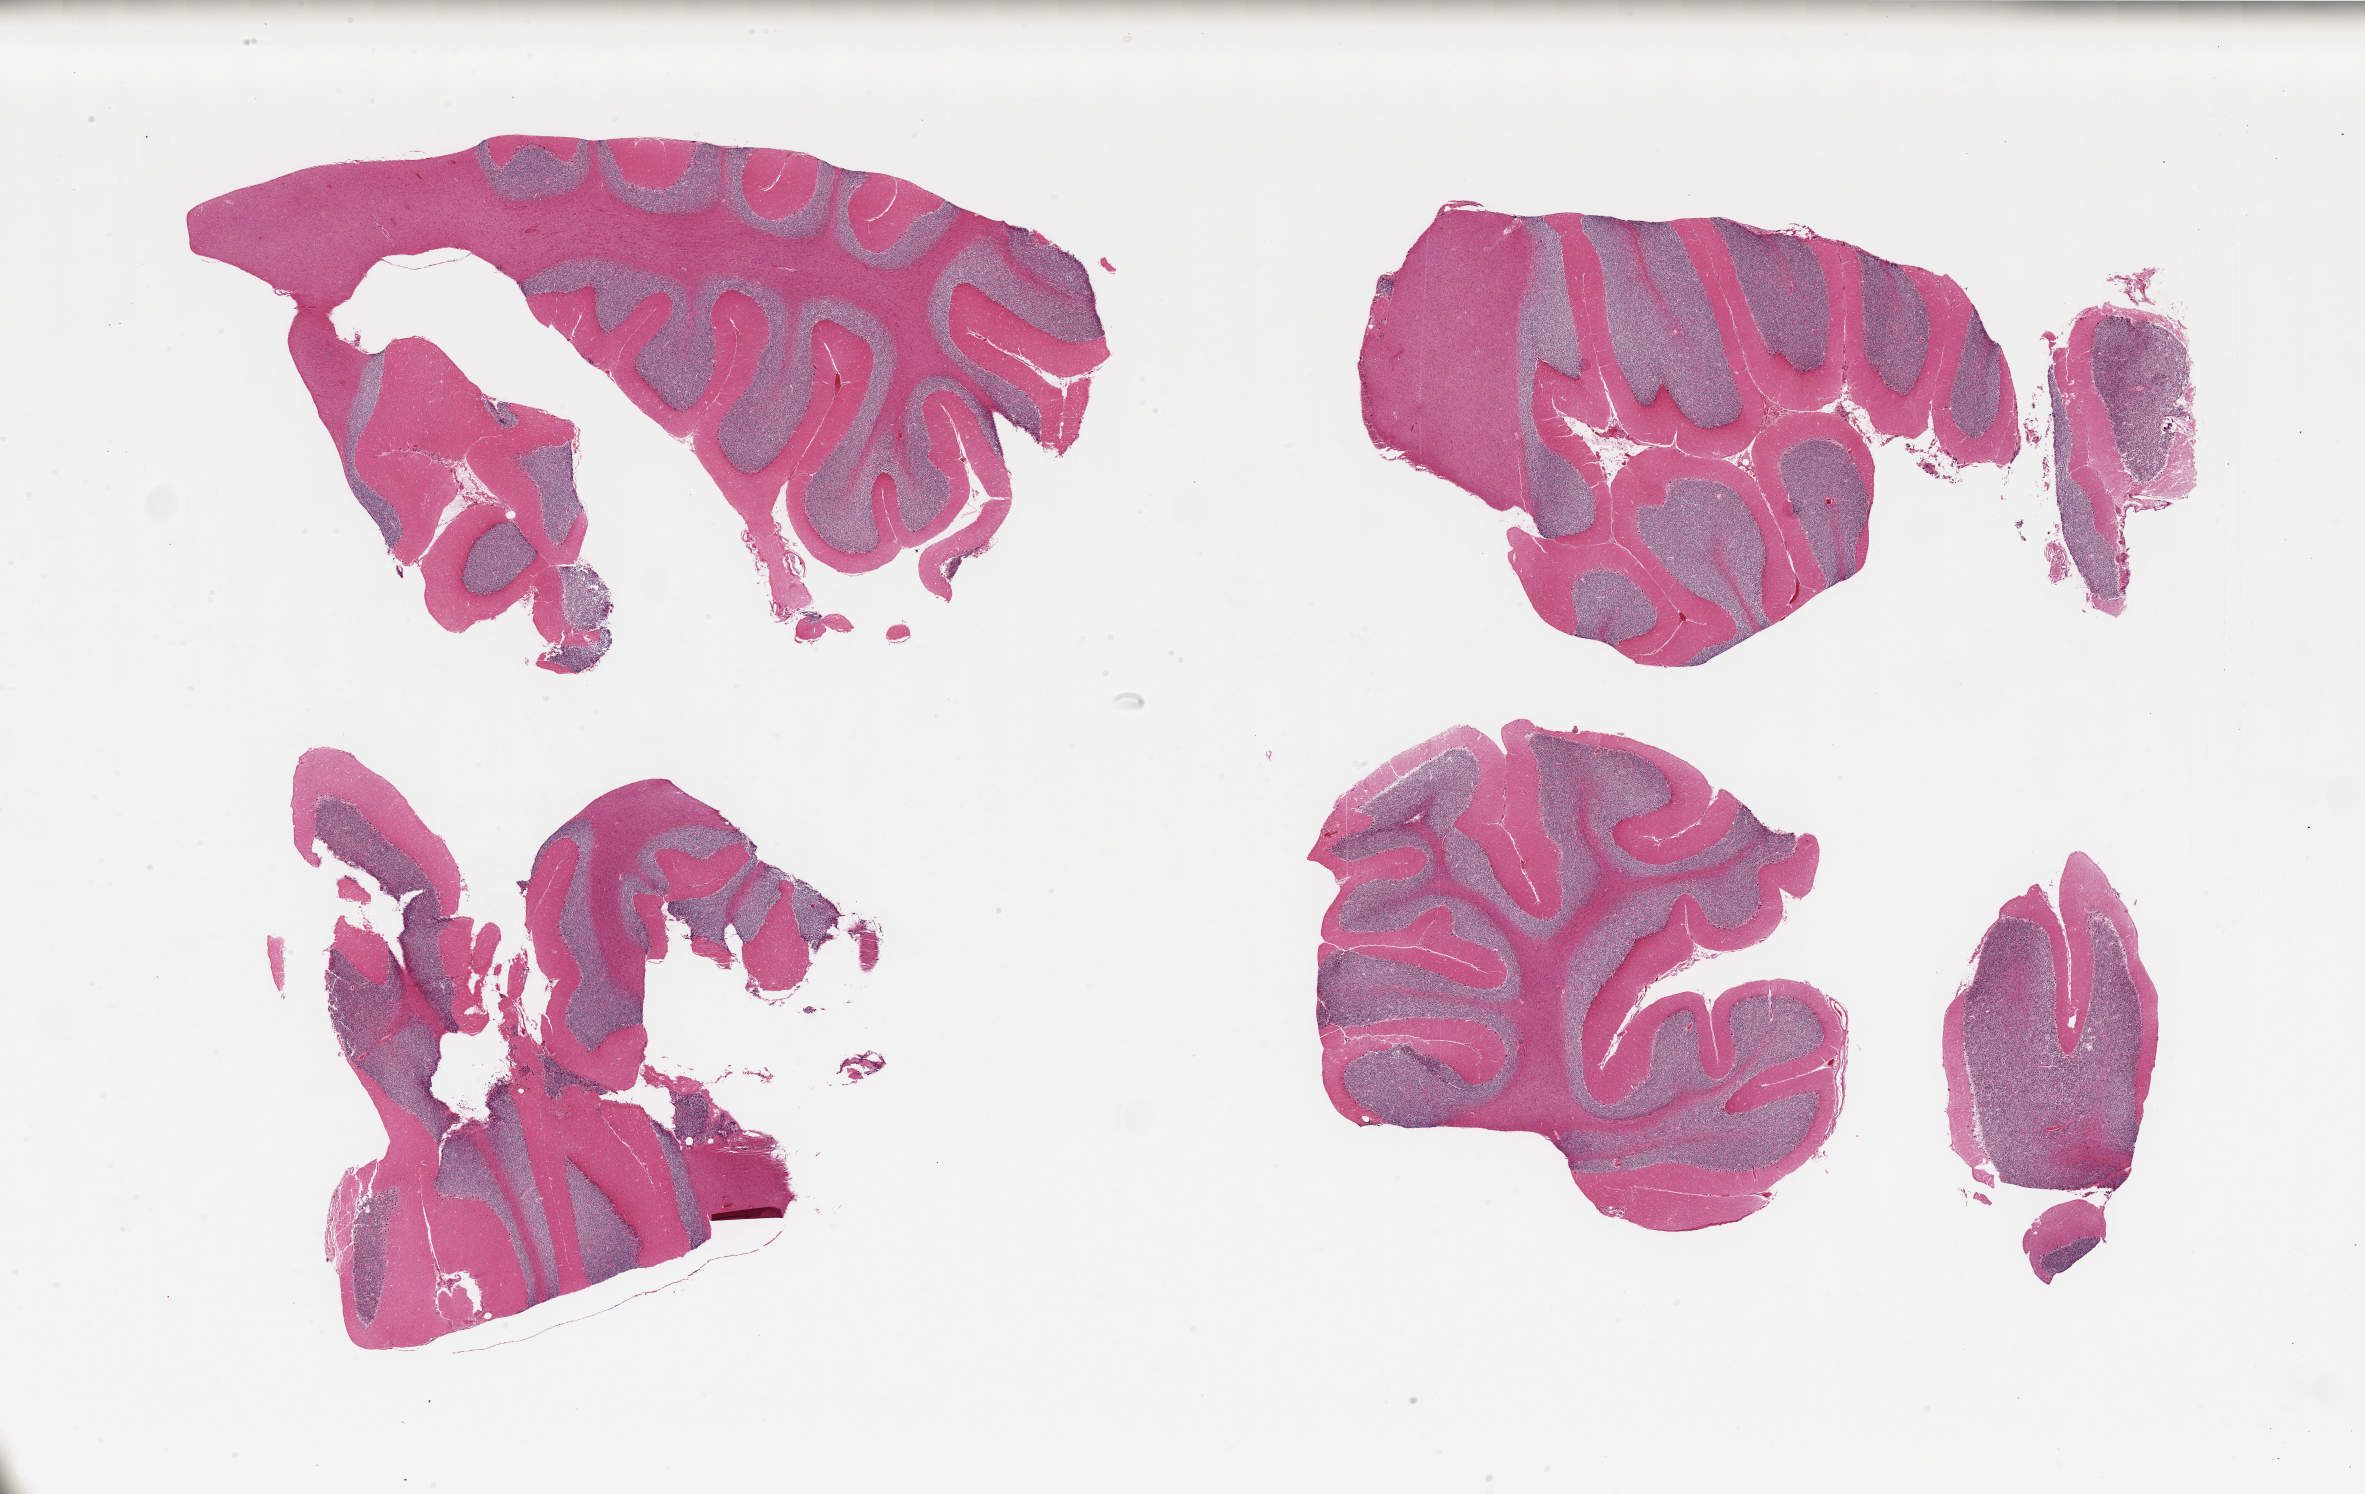
H&E whole-slide image — a low-resolution overview of the entire scanned area, about 37.4 x 23.6 mm (from a 20x scan); PAXgene-fixed, paraffin-embedded tissue; section of cerebellum (target tissue); tissue donor sample.
* review note (as recorded): 4 pieces; Purkinje cells present